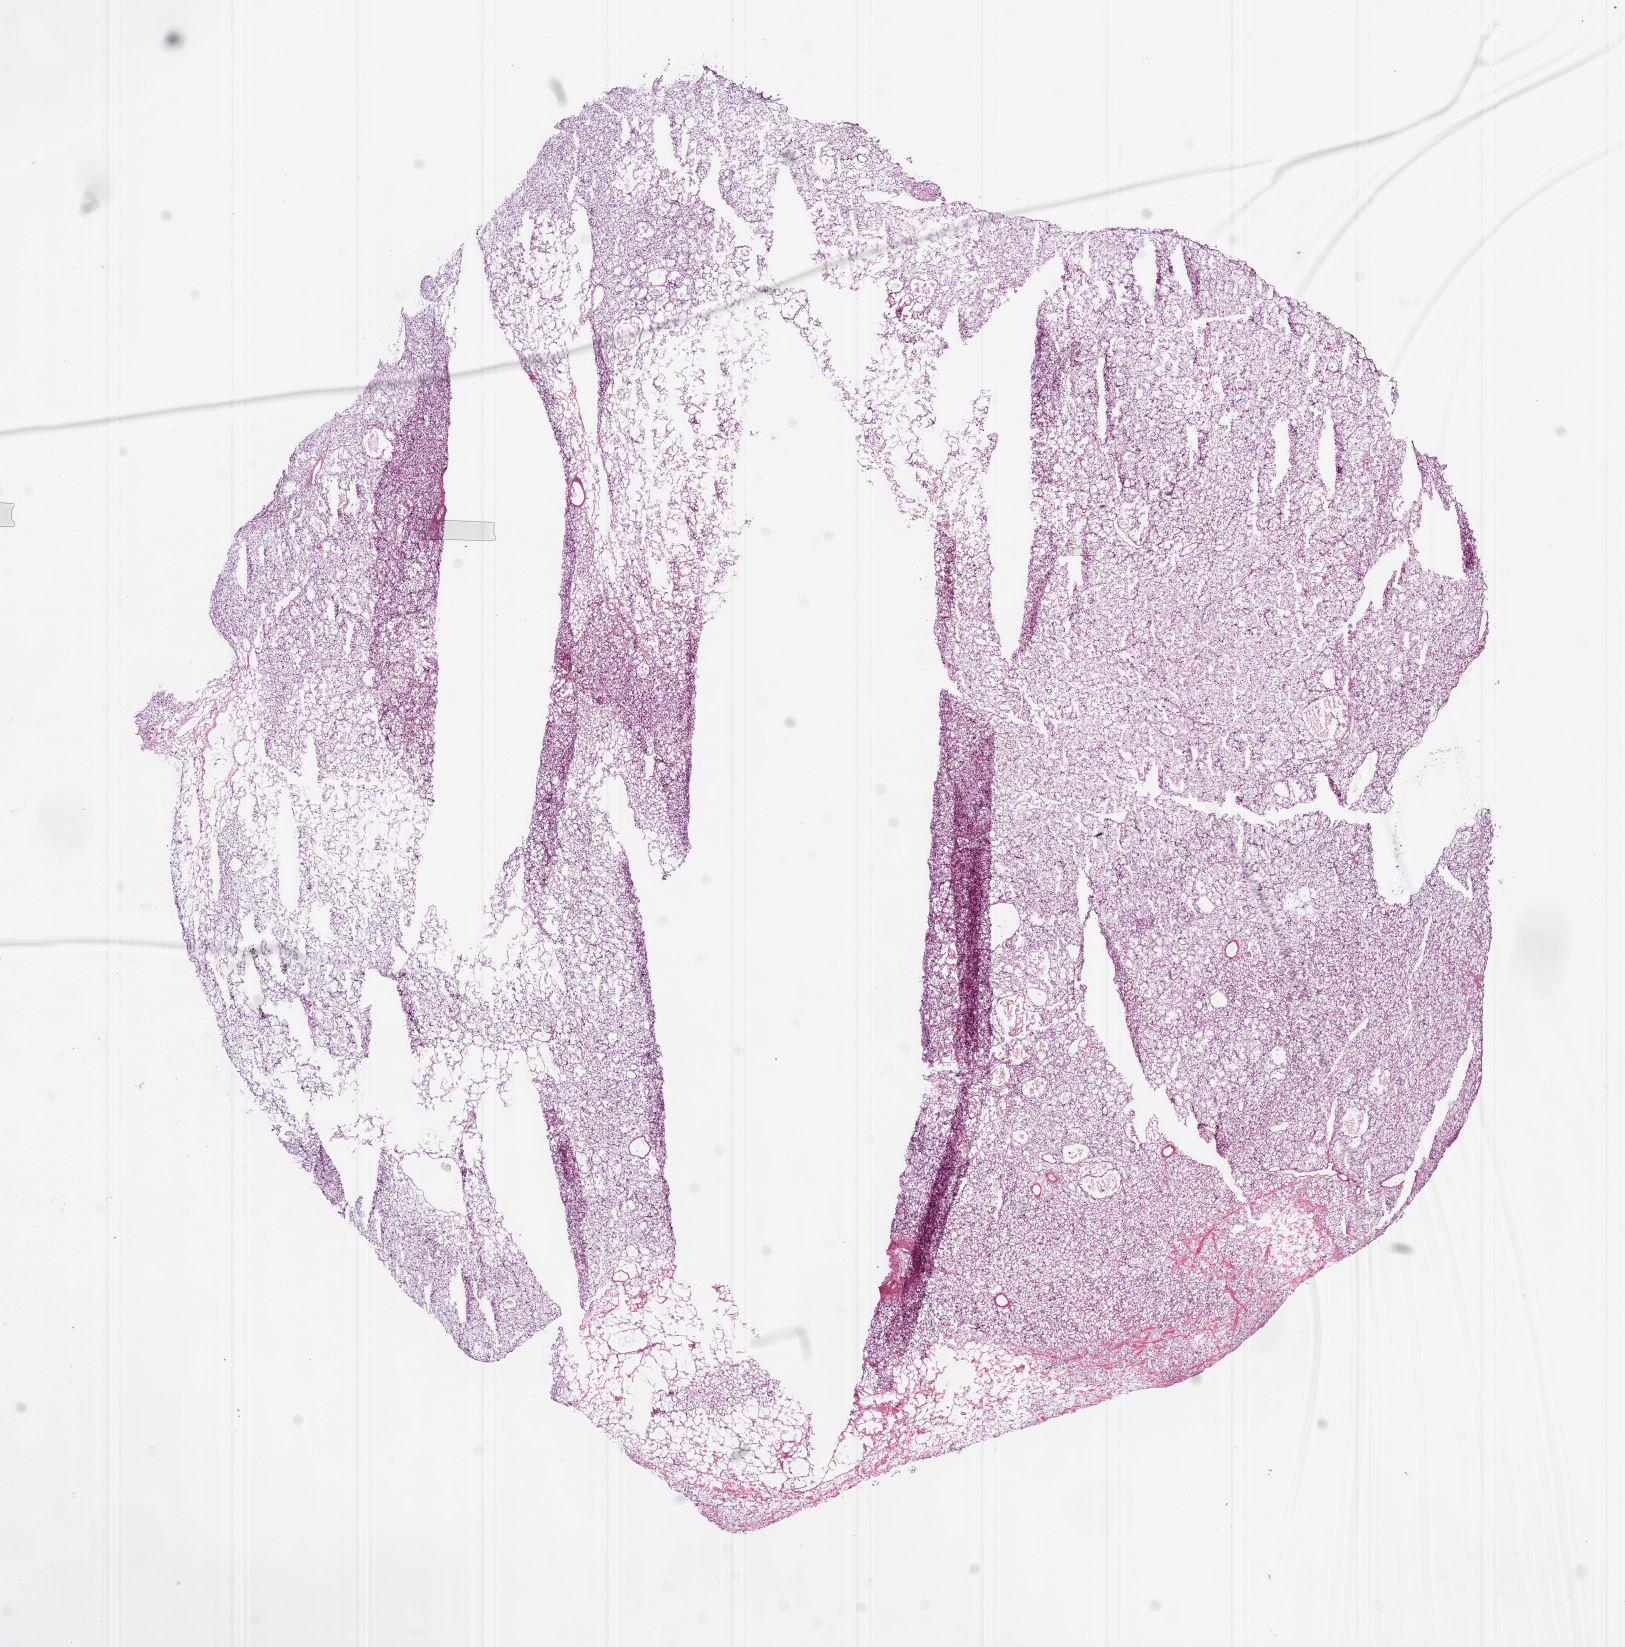
Digitized H&E-stained tissue section (whole slide), shown as a low-resolution overview of the whole scanned area (about 13.0 x 13.2 mm), frozen section, kidney, primary tumour sample. Female, age 50 years at initial diagnosis. Histologic grade: G2 (moderately differentiated). Slide review estimates, as recorded: tumour cells 95%, tumour nuclei 90%, normal cells 0%, stromal cells 5%, necrosis 0%.
AJCC pathologic stage: I. Lymph nodes positive (case pathology): 0 of 1 examined. Histologic diagnosis: Clear cell adenocarcinoma, NOS.